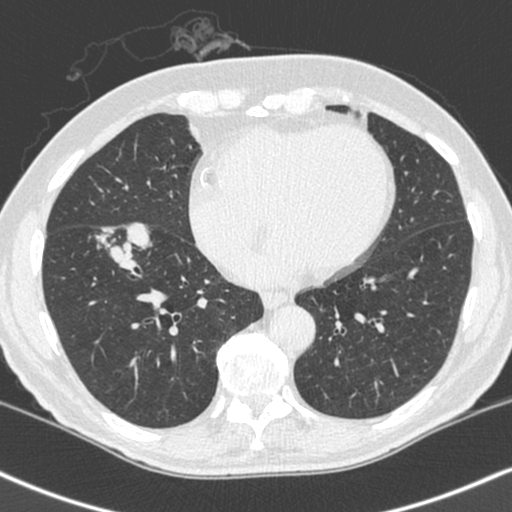
Low-dose screening chest CT, axial slice. Baseline screening round. Lung window (W 1500 / L -600 HU). Standard (soft-tissue) reconstruction kernel (C). 120 kVp. Slice 147 of 248 in the series. 512 × 512 image matrix, field of view 323 × 323 mm. Male, age 68 years at enrolment. Current smoker at enrolment.
• Expert reader's lesion annotation, bounding box [x1, y1, x2, y2] px = [85, 219, 160, 289].
• The exam's reader record, not a measurement of the box and not confirmed to be the same lesion: non-calcified nodule or mass ≥4 mm, right lower lobe, 34 × 17 mm, smooth margins, soft tissue attenuation.
• Participant outcome: lung cancer diagnosed 24 days after this screen — combined small cell carcinoma, right lower lobe, stage IIIA (AJCC 6th edition), 41 mm at pathology.